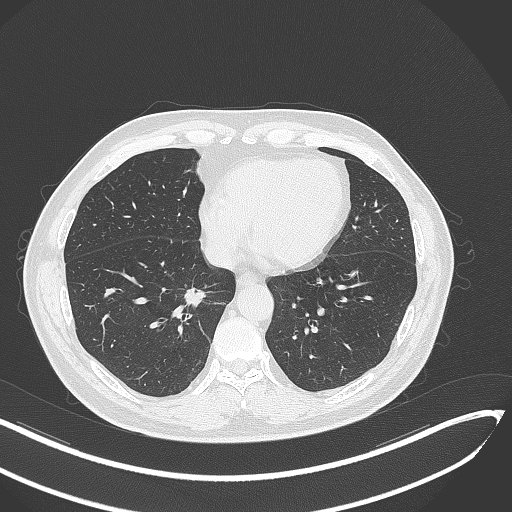
Chest CT, one axial slice; slice 130 of 429 in the series (ordered by position); lung window (W 1500 / L -600 HU); 512 × 512 image matrix. Male patient, age 62 years. From the clinical record (not read from this slice): clinical TNM (as recorded): T1b N0 M0.
Outlined on this slice (bounding box drawn by a radiologist):
- lung tumour (recorded histology: adenocarcinoma): bounding box [x1, y1, x2, y2] px = [183, 285, 218, 308]